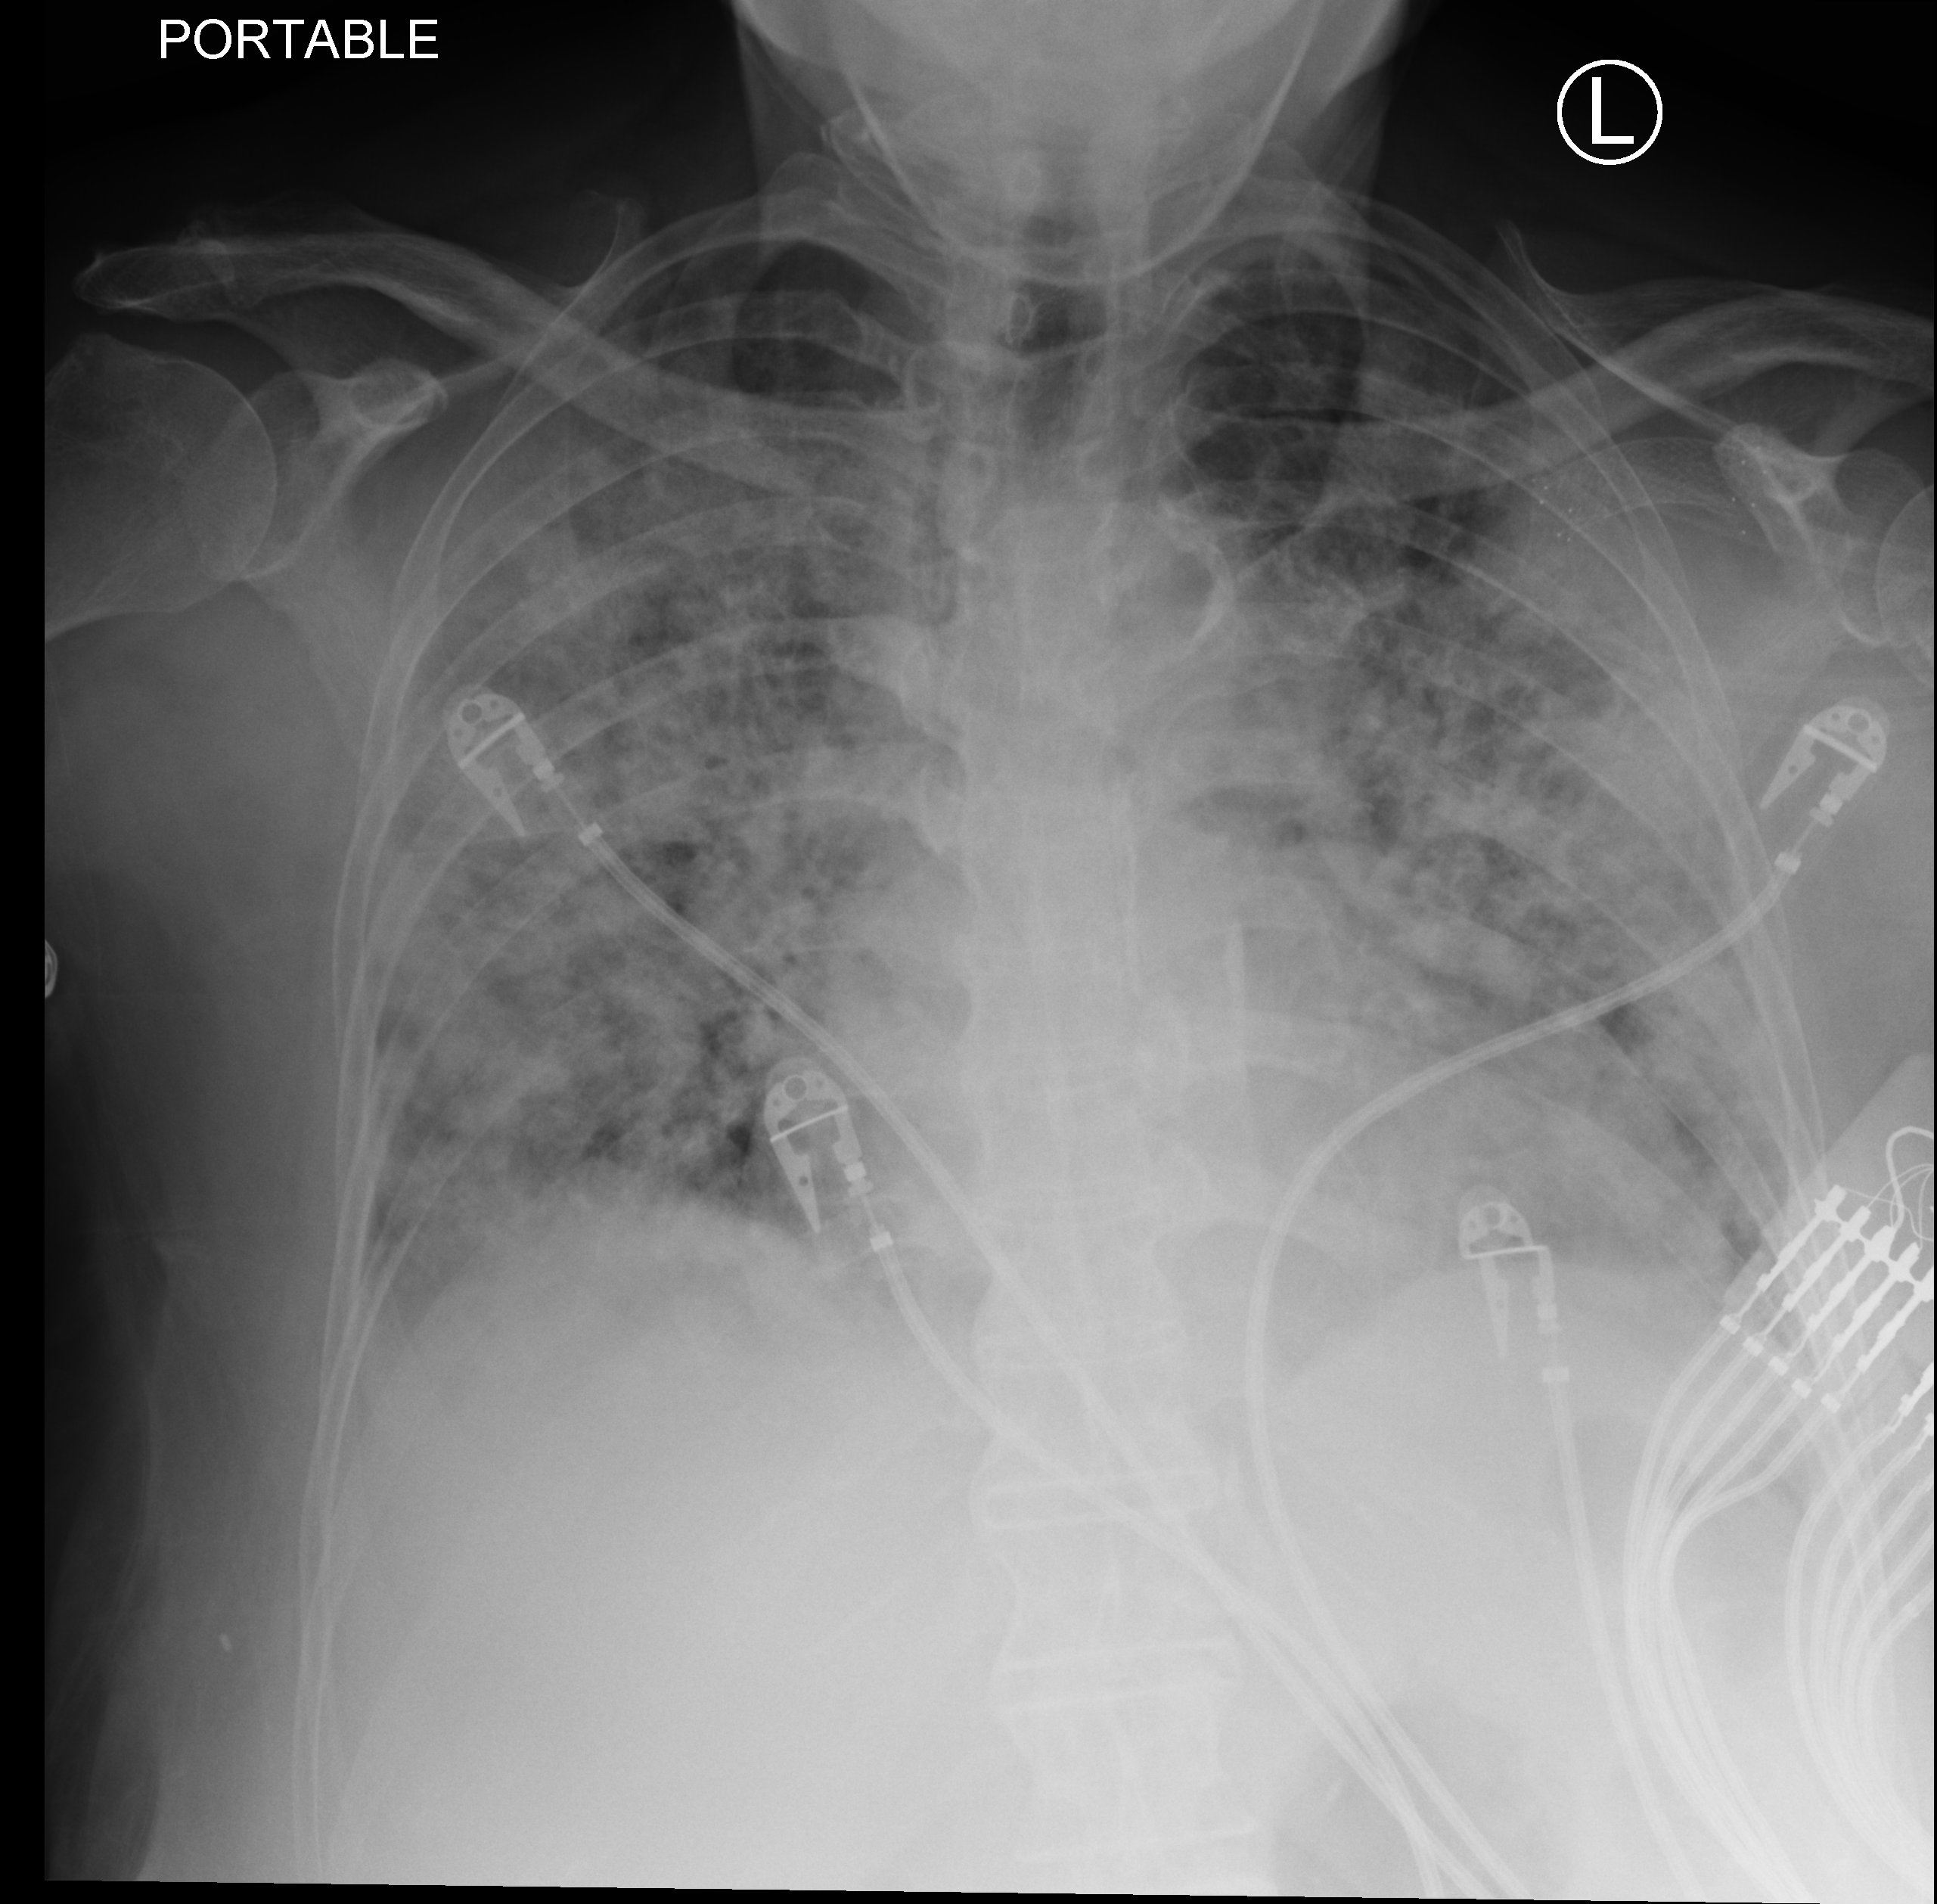
Bedside chest radiograph (computed radiography), anteroposterior (AP) projection. Female patient hospitalised with COVID-19, age 60–74 years.
Admission-level facts for this patient (not findings on this image; timing relative to this image not recorded): admitted to intensive care during this hospital stay: yes; chronic kidney disease (admission record): no; COPD (admission record): no.